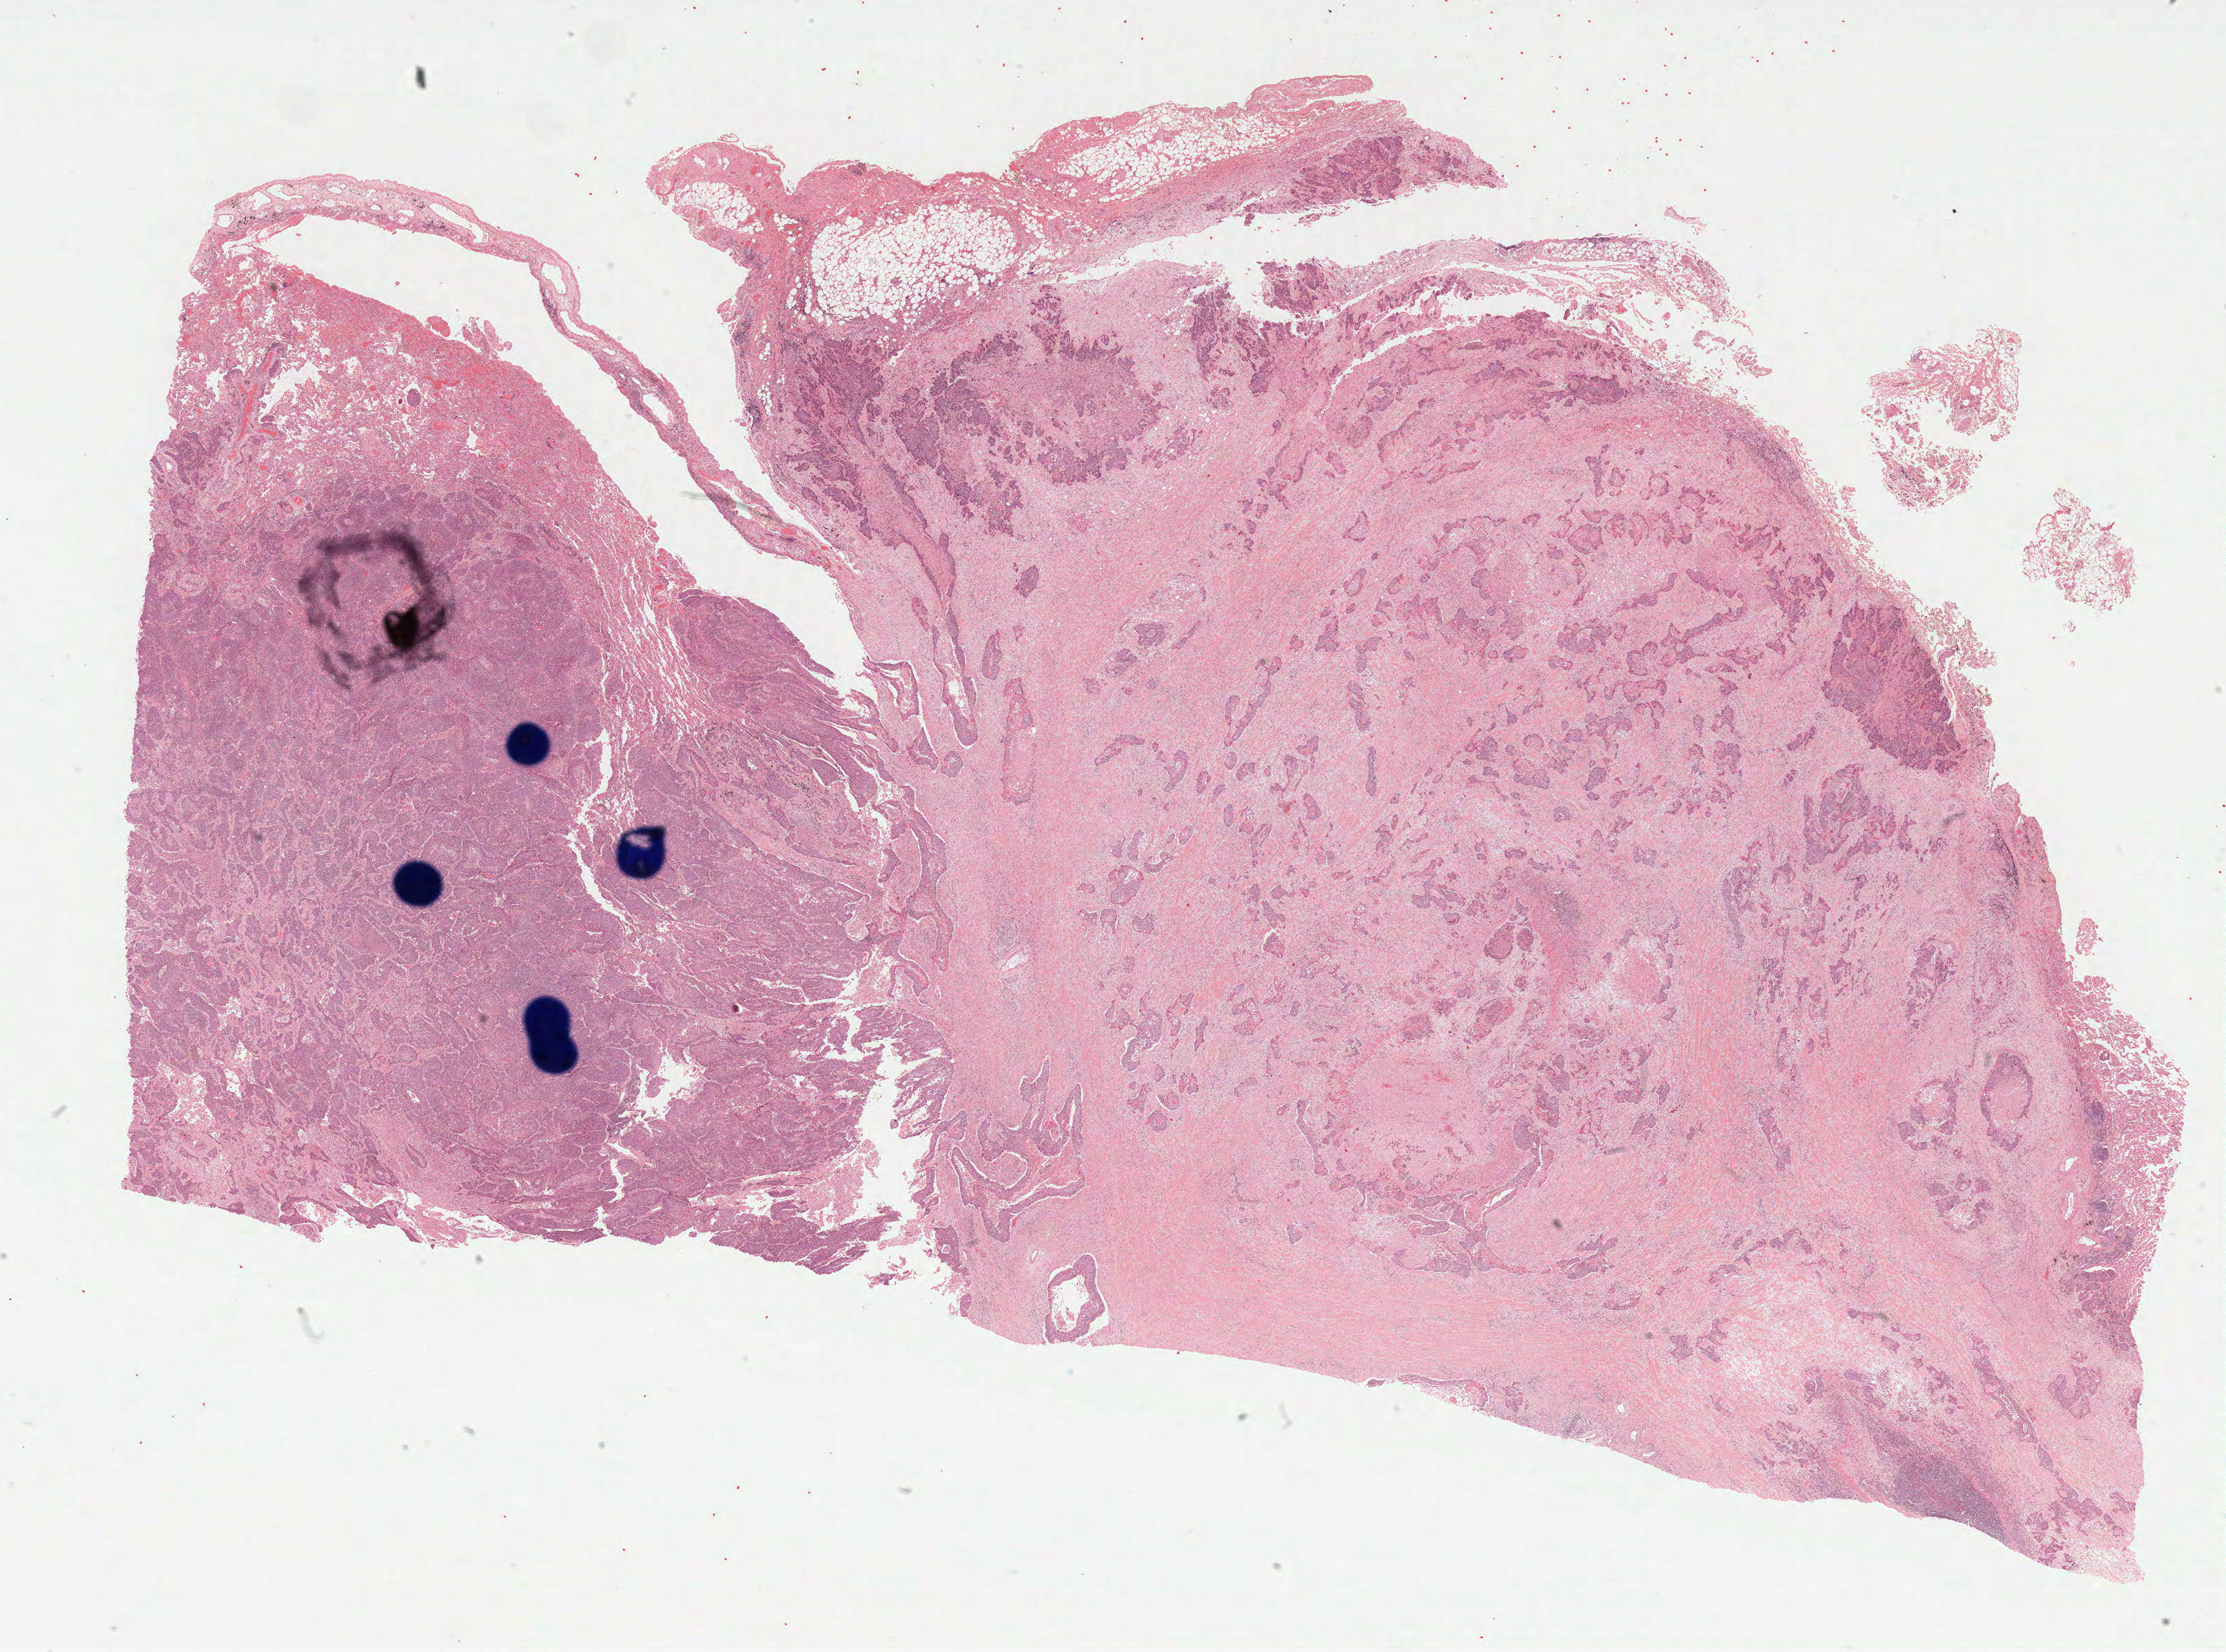
Digitized H&E tissue section (whole slide) — low-resolution overview of the scanned area, about 26.1 x 19.3 mm, formalin-fixed paraffin-embedded (FFPE) diagnostic section, sample: primary tumour, lung. Male, age 52 years at initial diagnosis.
Diagnosis: Squamous cell carcinoma, NOS (lower lobe, lung).